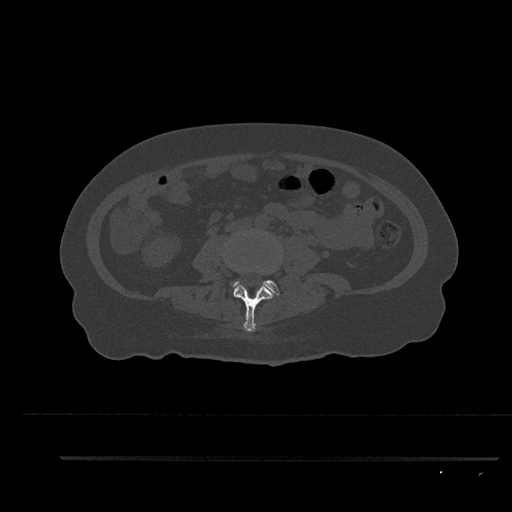
CT including the spine, one axial slice. Slice 60 of 797 in the series (ordered by position). Bone window (W 1800 / L 400 HU). 512 × 512 image matrix. Female patient, age 44 years. From the clinical record (not read from this slice): primary cancer: renal; vertebrae with lytic lesions (as recorded): L1.
Annotated regions visible in this slice (semi-automatic segmentation, software-assisted and operator-edited):
- L3 vertebra: bounding box [x1, y1, x2, y2] px = [233, 282, 278, 331]
- L4 vertebra: [233, 280, 280, 295]